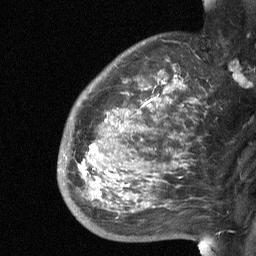
Breast MRI (dynamic contrast-enhanced), one sagittal slice; position 47 of 64 along the scan axis; dynamic contrast-enhanced study with each time point stored as its own series, time point 2 of 3 at this slice position (early post-contrast, ordered by acquisition time); 1.5 T; TE 4.8 ms, TR 27 ms; 2 mm slice thickness; 256 × 256 image matrix, field of view 200 × 200 mm. Female patient, age 50 years. From the clinical record (not read from this slice): setting: breast cancer imaged before/during neoadjuvant chemotherapy; receptor status: HER2-positive.
Annotated regions visible in this slice (semi-automatically segmented with operator editing):
- analysis volume of interest (the breast-tissue region the enhancement analysis was run in; not a lesion): bounding box <57,91,203,227> (left, top, right, bottom; pixels)
- tumour enhancement mask (voxels above the 90 % enhancement threshold inside the analysis volume of interest): <79,145,95,174>